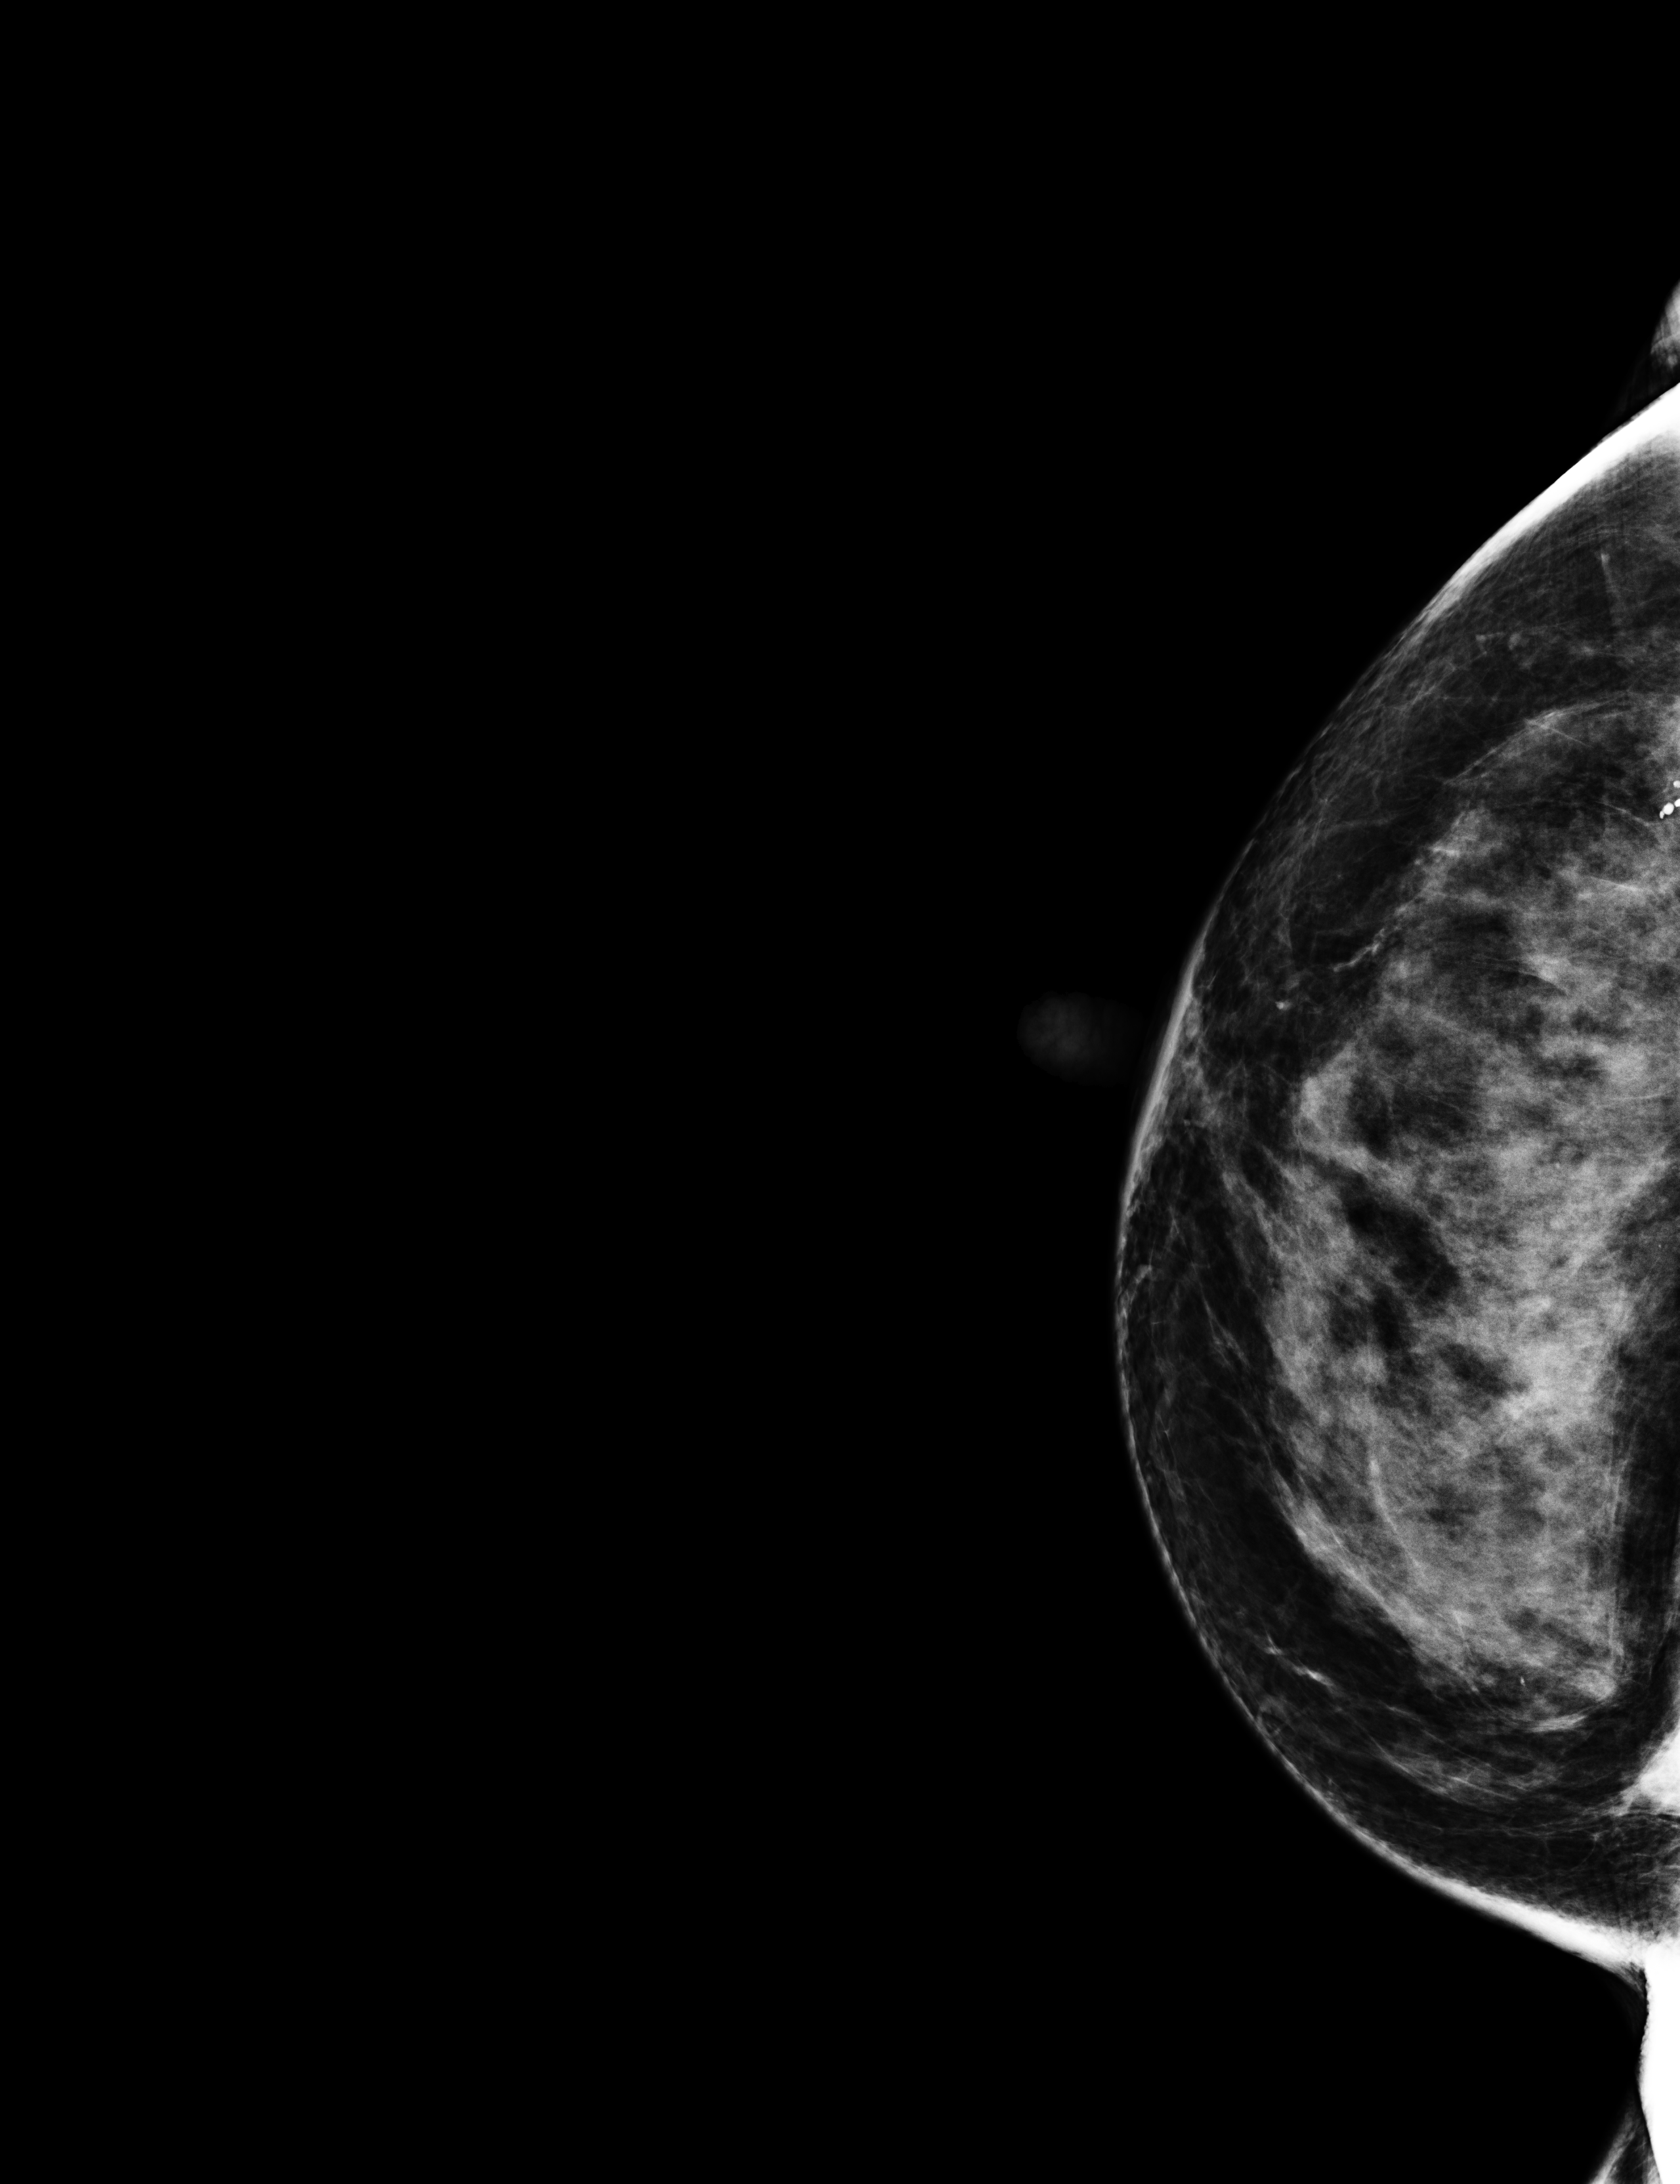
Digital mammogram (FFDM), right breast, craniocaudal (CC) view, annual screening mammography examination, compressed breast thickness 79 mm, system: Selenia Dimensions. Female patient, age 53 years.
Breast density at the screening exam (both breasts): extremely dense (BI-RADS density category d). Final BI-RADS assessment for this screening round (tomosynthesis exam, both breasts): category 2. Recall: no recall after this screen.